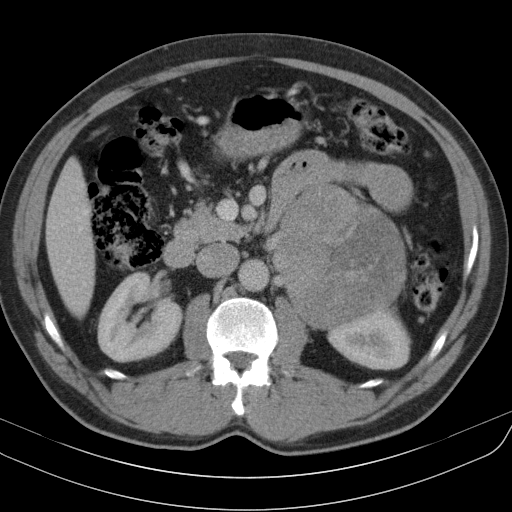
Contrast-enhanced abdominal CT, one axial slice. Position 60 of 91 along the scan axis. 130 kVp. Intravenous contrast given. Soft-tissue window (W 400 / L 40 HU). 512 × 512 image matrix, field of view 370 × 370 mm. Patient: male, 51 years. From the clinical record (not read from this slice): diagnosis: adrenocortical carcinoma; tumour side: left adrenal.
Annotated regions visible in this slice (semi-automatic segmentation, software-assisted and operator-edited):
- mass: bounding box <278,187,407,328> (left, top, right, bottom; pixels)